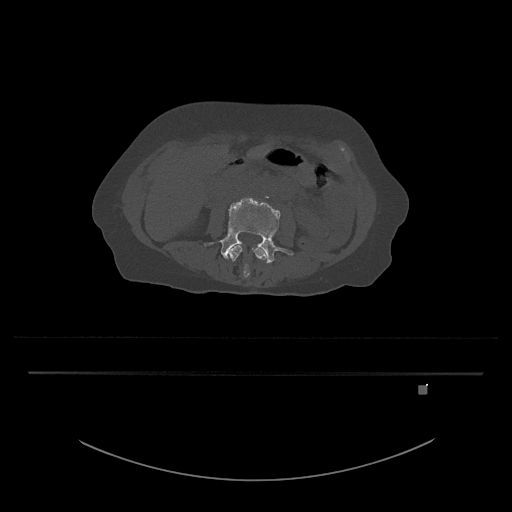
CT including the spine, one axial slice; position 385 of 797 along the scan axis; bone window (W 1800 / L 400 HU); 512 × 512 image matrix, field of view 500 × 500 mm. Patient: female, 57 years. Case-level facts recorded for this patient, not image findings: primary cancer: cervical.
Annotated regions visible in this slice (semi-automatically segmented with operator editing):
- L3 vertebra: bounding box (x1, y1, x2, y2) in pixels: (229, 244, 267, 278)
- L4 vertebra: (204, 198, 294, 264)